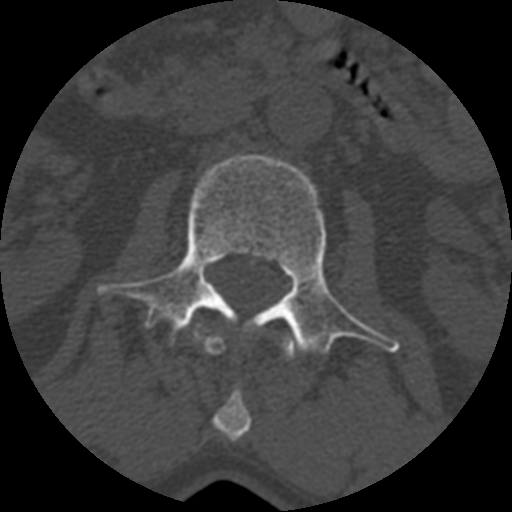
CT including the spine, one axial slice; slice 337 of 399 in the series (ordered by position); reconstruction kernel STANDARD; 120 kVp; bone window (W 1800 / L 400 HU); 1.25 mm slice thickness; 512 × 512 image matrix, field of view 160 × 160 mm. Patient age 71 years. From the clinical record (not read from this slice): primary cancer: prostate.
Outlined on this slice (semi-automatically segmented with operator editing):
- L1 vertebra: bounding box <194,332,295,439> (left, top, right, bottom; pixels)
- L2 vertebra: <97,154,400,355>